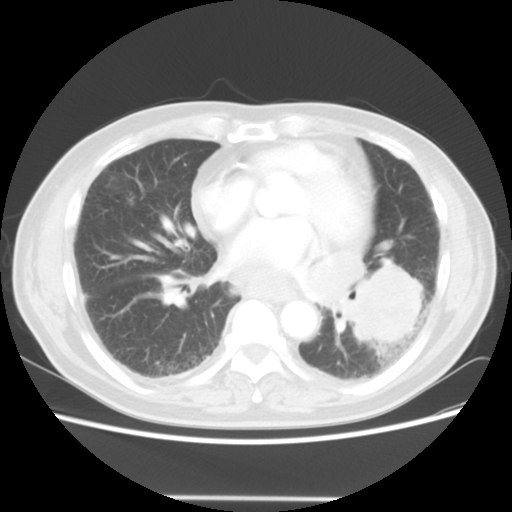
Chest CT, one axial slice; position 21 of 56 along the scan axis; reconstruction kernel STANDARD; 140 kVp; lung window (W 1500 / L -600 HU); 5 mm slice thickness; 512 × 512 image matrix, field of view 360 × 360 mm. Male patient, age 66 years. Case-level facts recorded for this patient, not image findings: clinical TNM (as recorded): T4 N3 M0.
Outlined on this slice (bounding box drawn by a radiologist):
- lung tumour (recorded histology: small cell carcinoma): bounding box (x1, y1, x2, y2) in pixels: (342, 255, 429, 353)